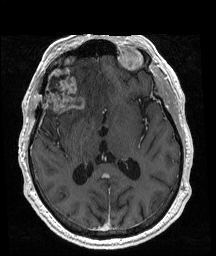
Brain MRI from a brain-tumour surgery series, one axial slice; slice 98 of 192 in the series (ordered by position); T1-weighted post-contrast; 1 mm slice thickness; 216 × 256 image matrix. Case-level facts recorded for this patient, not image findings: histopathology: Glioblastoma; WHO grade: 4; IDH mutation: no; tumour location: Right Frontal.
Structures marked on this image (manually delineated by an expert):
- previous resection cavity: bounding box [x1, y1, x2, y2] px = [49, 76, 64, 94]